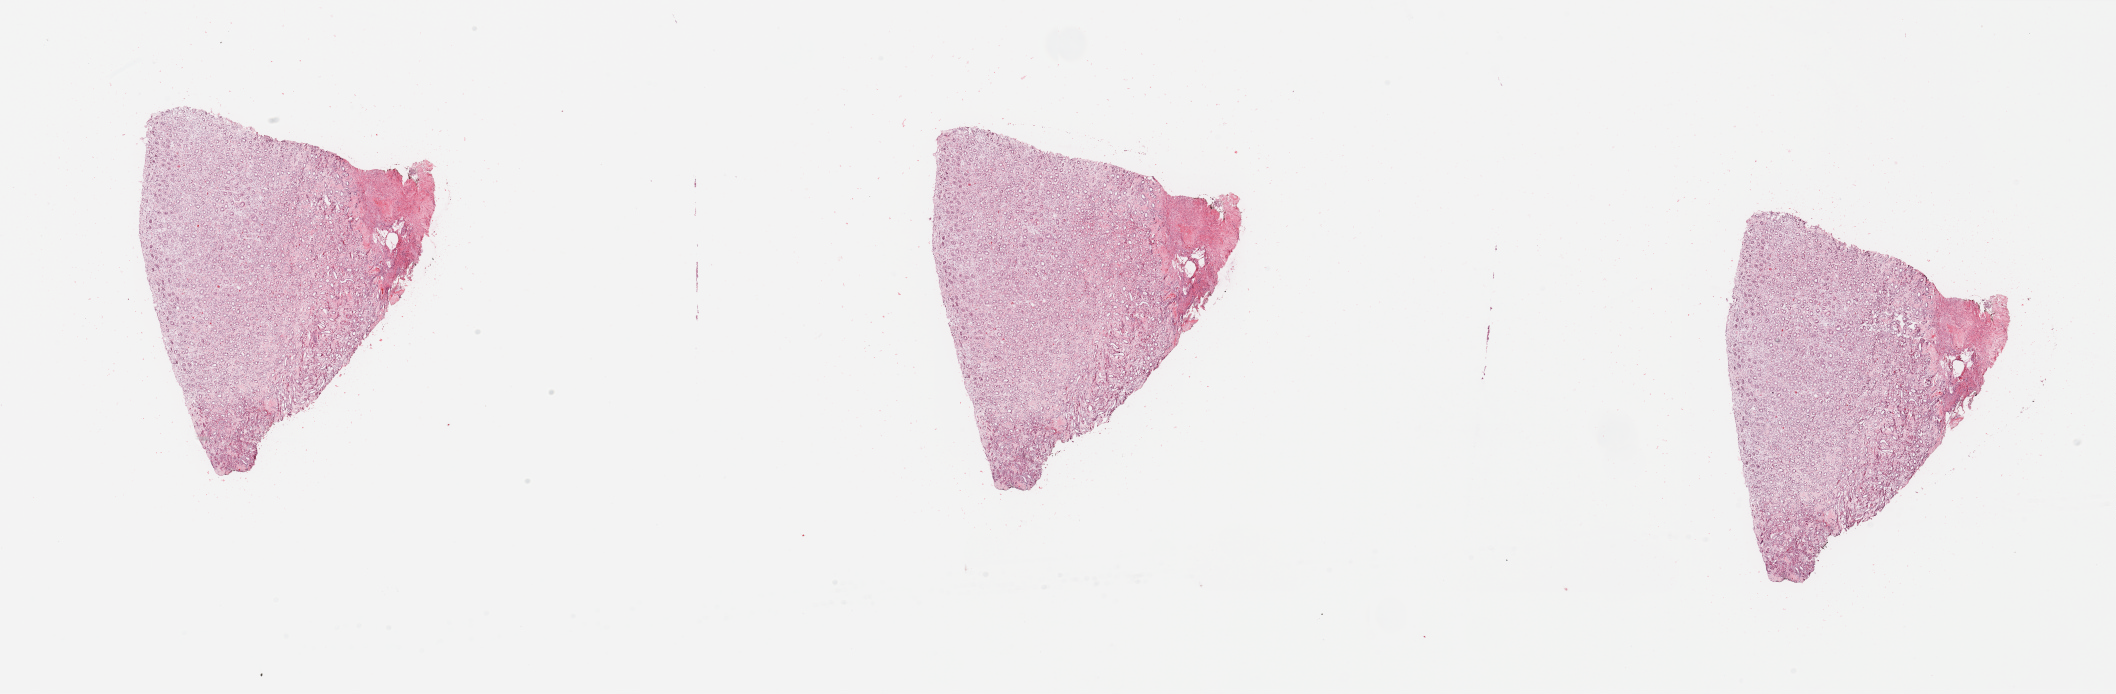
Hematoxylin and eosin (H&E) stained whole-slide image — low-resolution overview of the scanned area, about 33.5 x 11.0 mm. Normal (non-tumour) tissue sample, kidney. Male, 62 y/o.
This section: normal (non-tumour) tissue from the same patient. Patient diagnosis: Renal cell carcinoma, NOS.